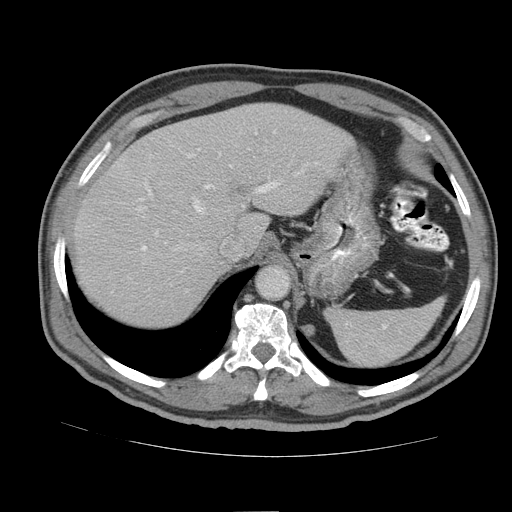
Contrast-enhanced abdominal CT (liver protocol), one axial slice. Position 66 of 105 along the scan axis. Reconstruction kernel STANDARD. Soft-tissue window (W 400 / L 40 HU). 512 × 512 image matrix, field of view 380 × 380 mm. Case-level facts recorded for this patient, not image findings: diagnosis: hepatocellular carcinoma (patient treated with transarterial chemoembolisation; whether this scan precedes or follows treatment is not stated here); TNM stage (as recorded): Stage-IIIB; Child-Pugh class: A; tumour nodularity: multinodular.
Structures marked on this image (semi-automatic segmentation, software-assisted and operator-edited):
- abdominal aorta: box from (x=257, y=267) to (x=289, y=298) px
- liver parenchyma outside the tumour (the mass and vessels are separate outlines, so this box may not span the whole liver): (x=72, y=102)–(x=354, y=324)
- liver vessels: (x=140, y=131)–(x=279, y=250)